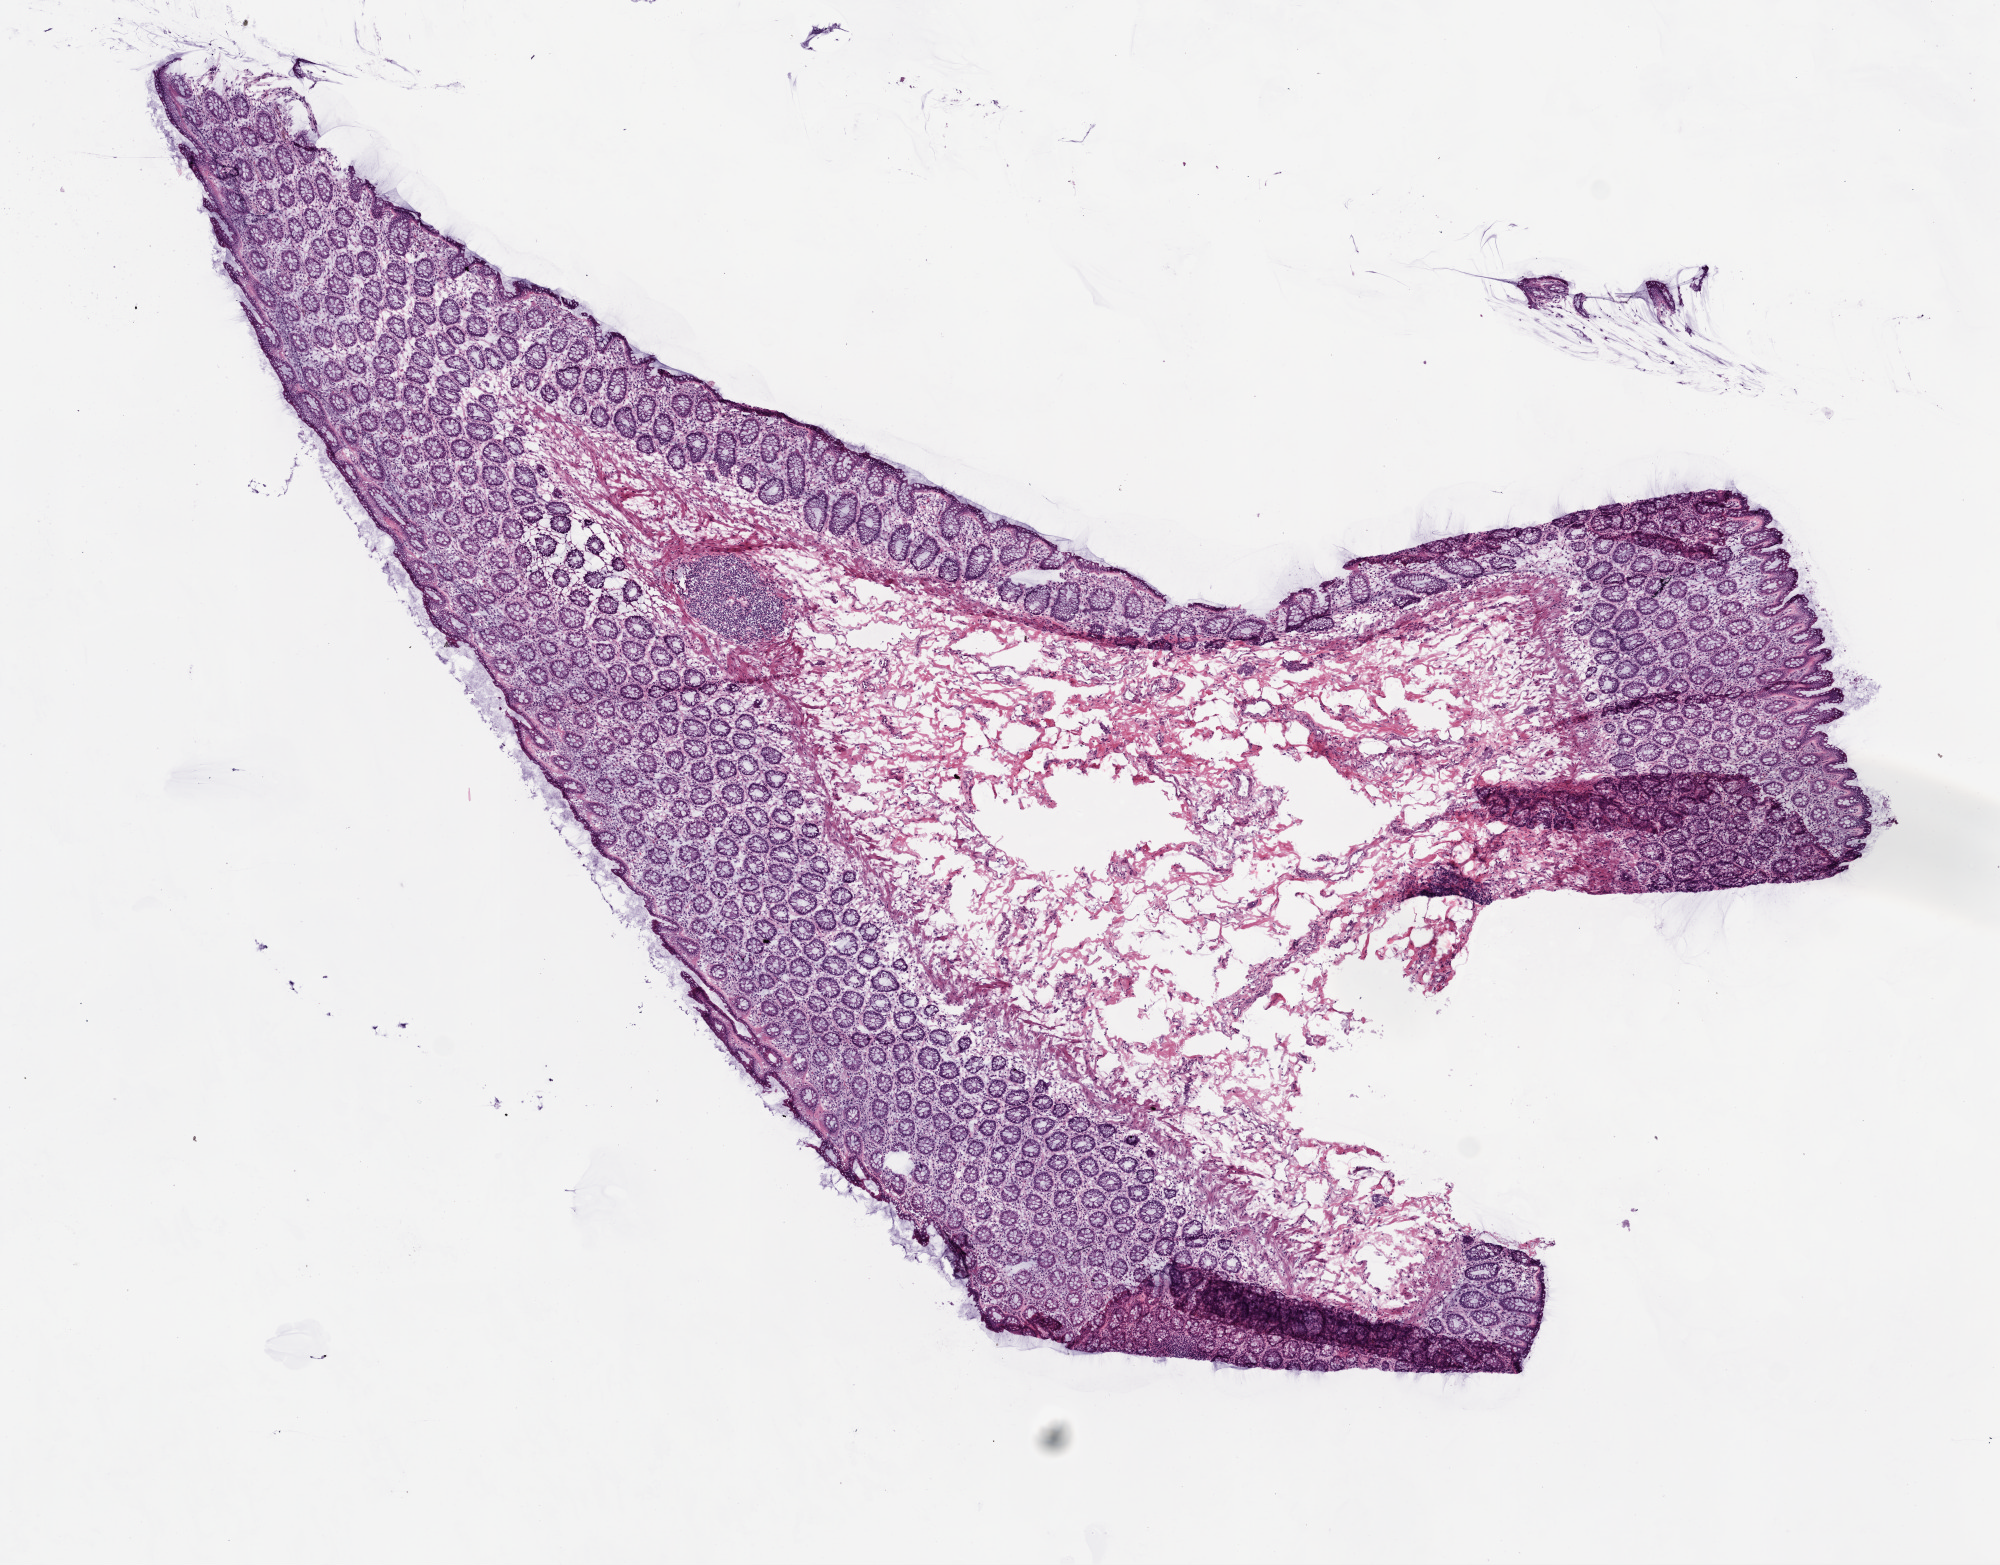
H&E-stained whole-slide image — low-resolution overview of the scanned area, about 8.0 x 6.3 mm (acquisition: 20x scan). Frozen section from the top of the tissue portion. Sample: solid tissue normal (non-tumour tissue), colon. Male patient; age at initial diagnosis 85 years.
This section: solid tissue normal (non-tumour) sample from the same patient. Patient diagnosis: Adenocarcinoma, NOS.